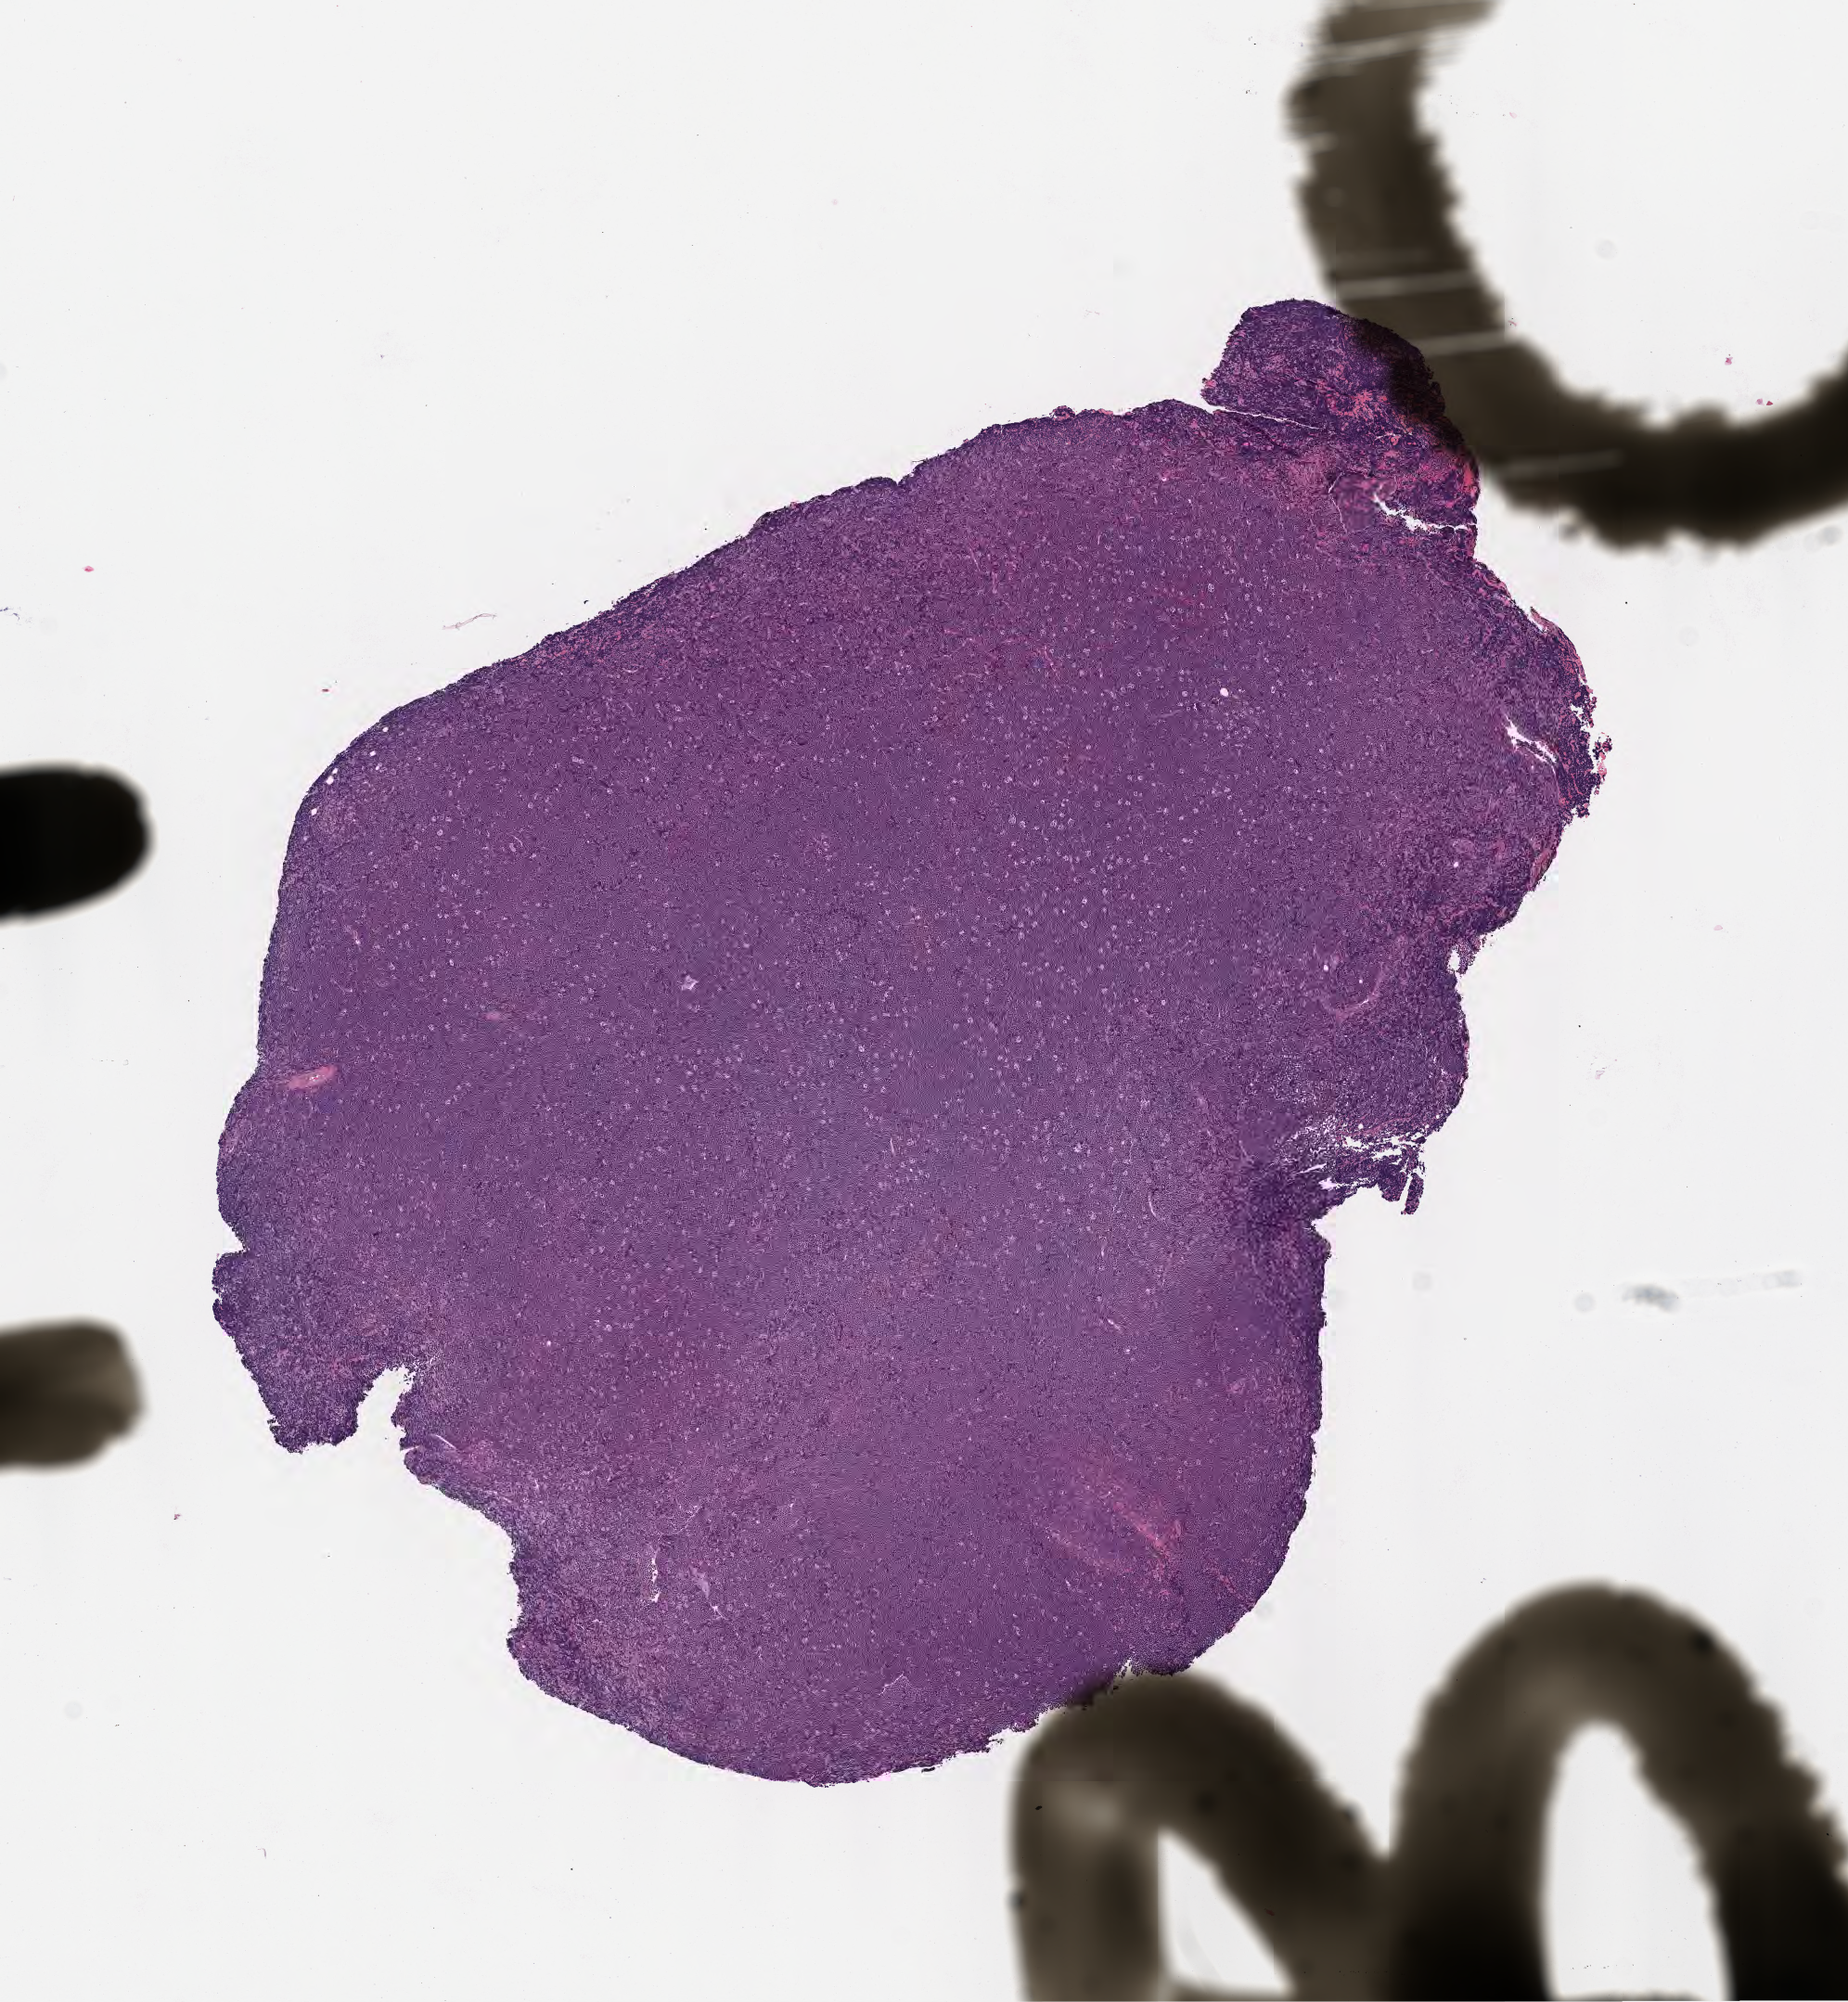
Digitized hematoxylin and eosin (H&E)-stained section — shown as a low-resolution overview of the whole scanned area (about 8.0 x 8.7 mm), specimen: tumor tissue, site: cranium. Male, age 2 years at initial diagnosis.
Histologic diagnosis: Burkitt lymphoma, NOS.